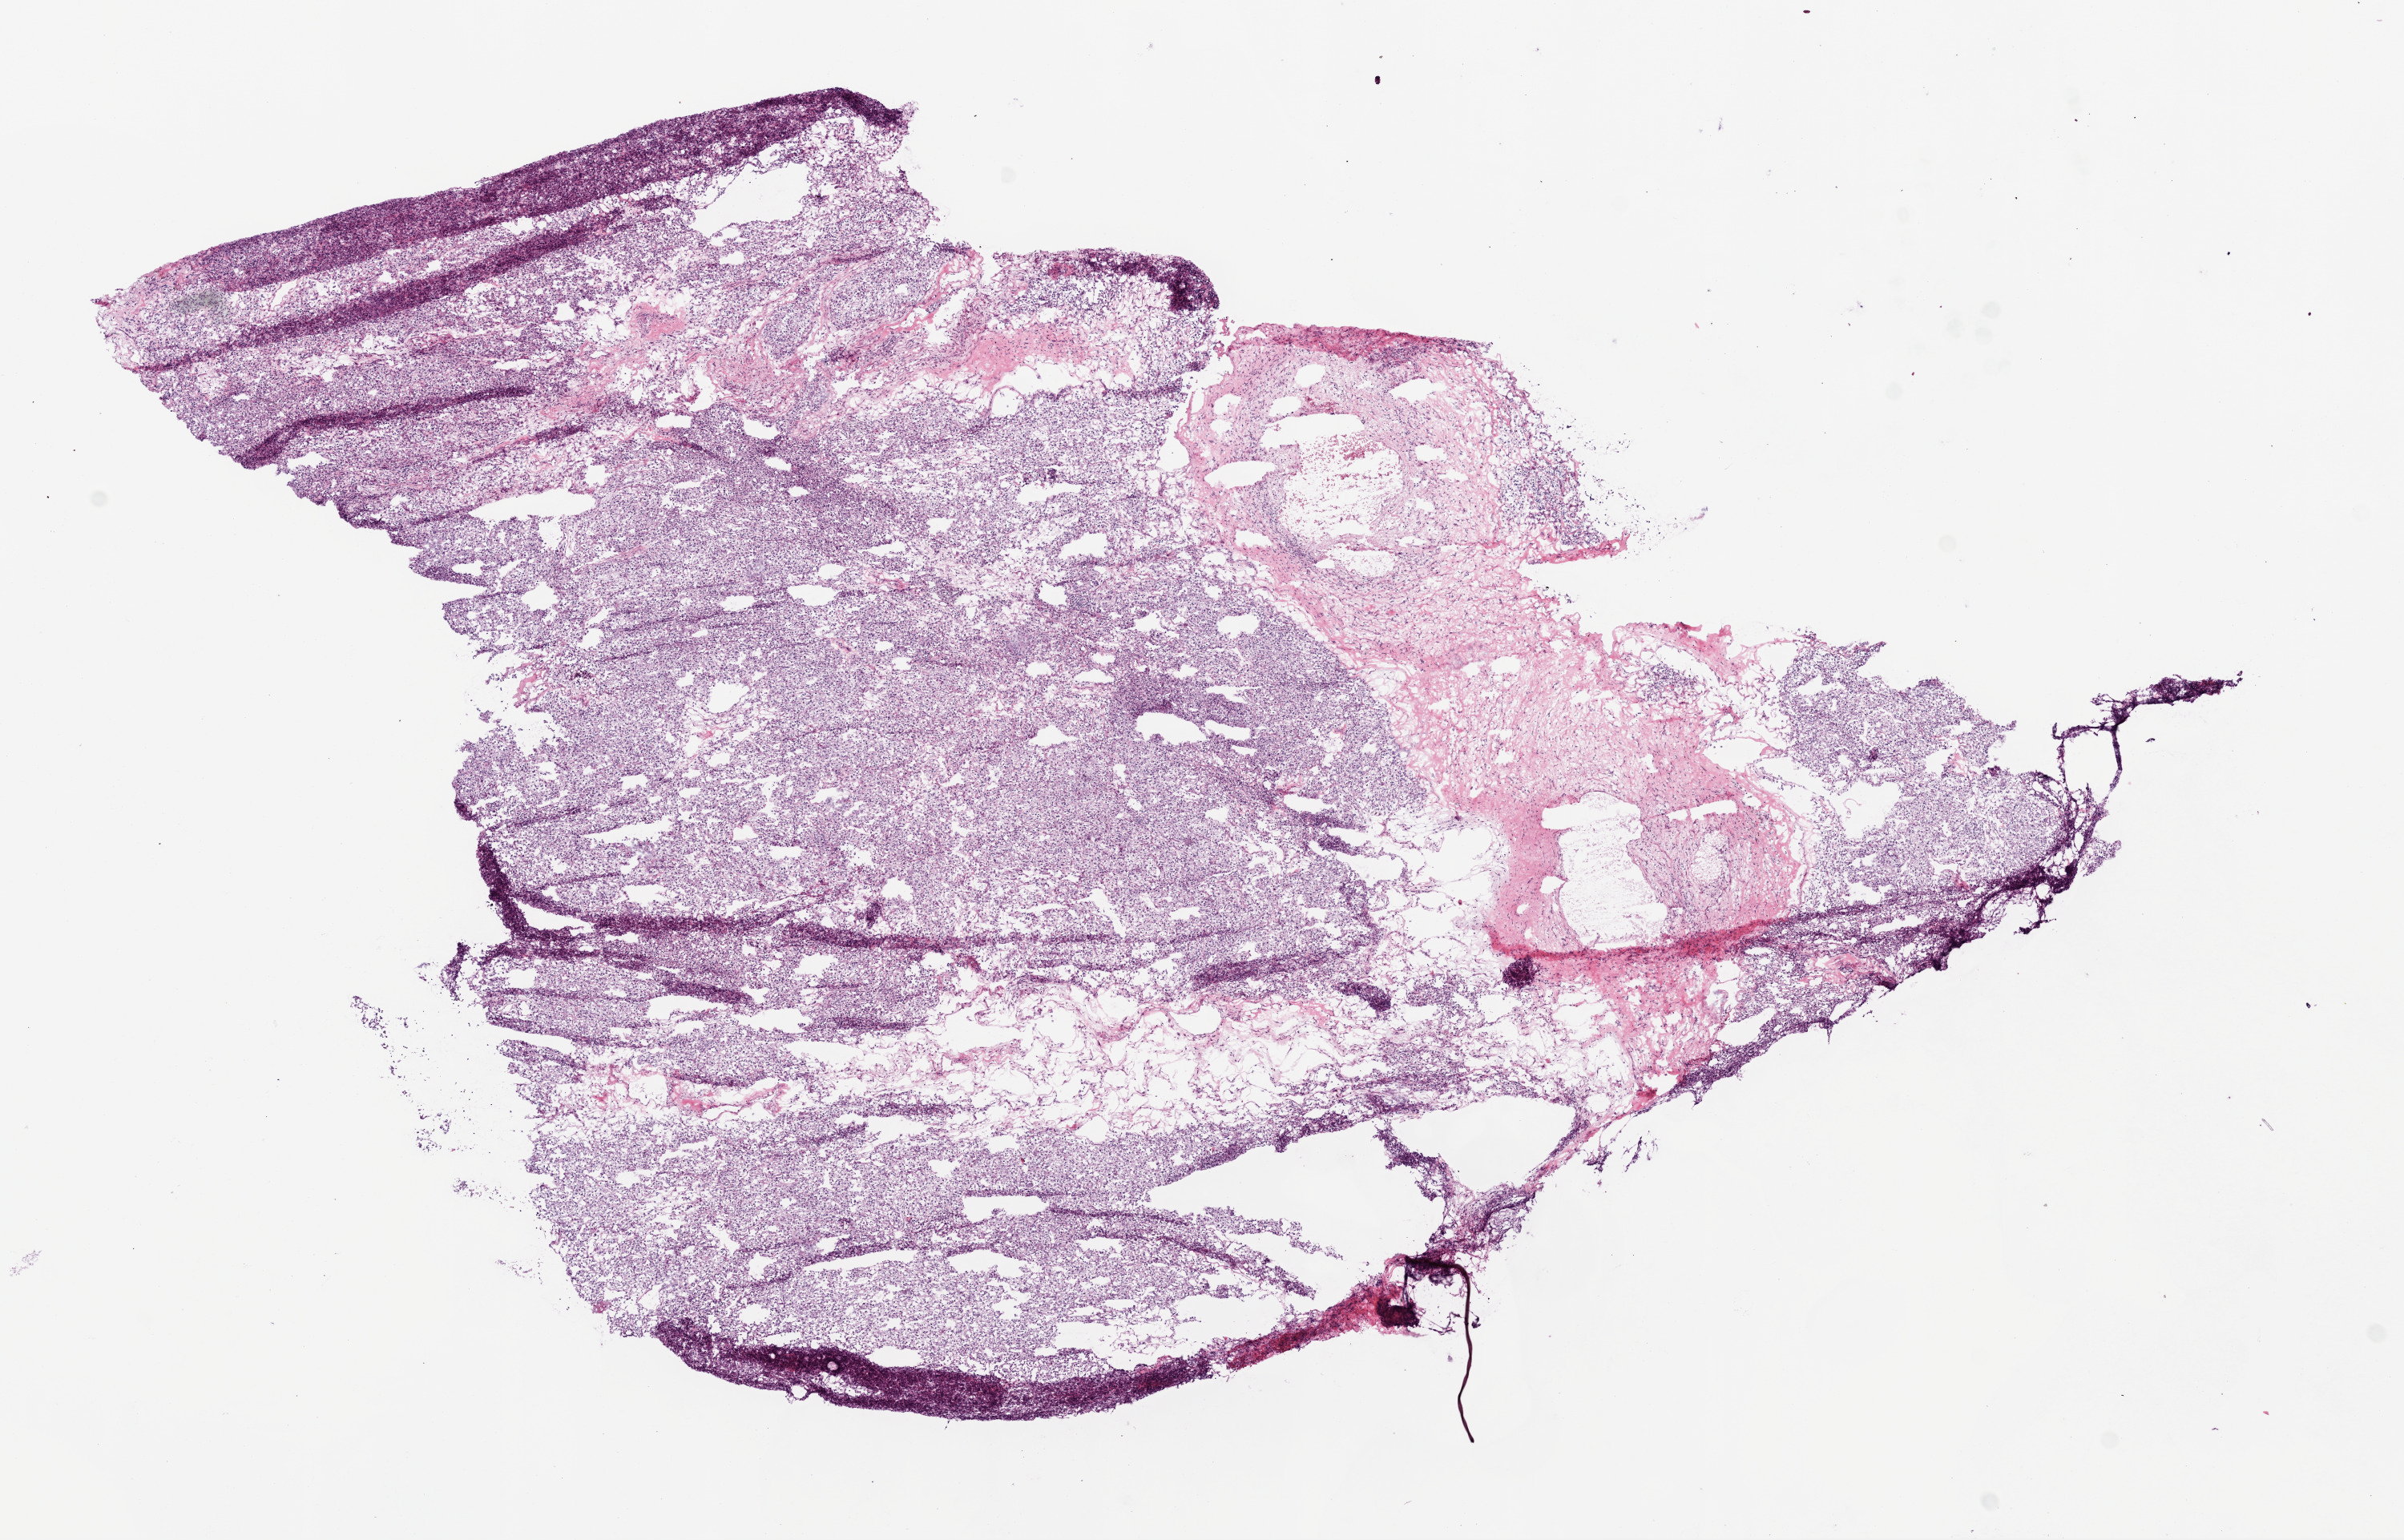
Whole-slide histology image, H&E-stained, shown as a low-resolution overview of the whole scanned area (about 12.0 x 7.7 mm); frozen section from the top of the tissue portion; primary tumour sample from the kidney. Male, age 64 years at initial diagnosis.
Pathologic diagnosis: Clear cell adenocarcinoma, NOS.